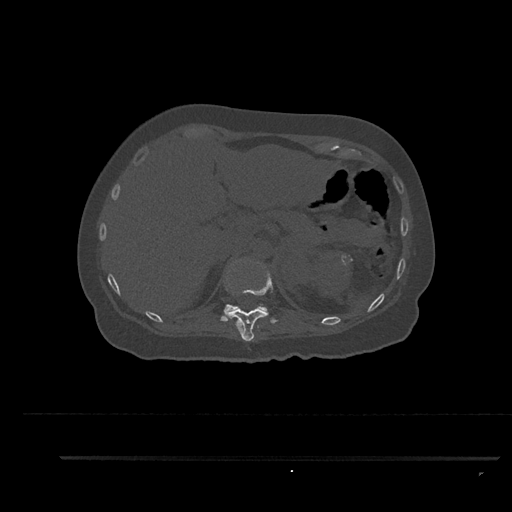
CT including the spine, one axial slice; position 296 of 797 along the scan axis; reconstruction kernel Br40s/3; 120 kVp; bone window (W 1800 / L 400 HU); 512 × 512 image matrix. Patient: female, 44 years. Case-level facts recorded for this patient, not image findings: primary cancer: renal.
Outlined on this slice (semi-automatically segmented with operator editing):
- T11 vertebra: bounding box (x1, y1, x2, y2) in pixels: (229, 262, 273, 341)
- T12 vertebra: (220, 259, 269, 322)